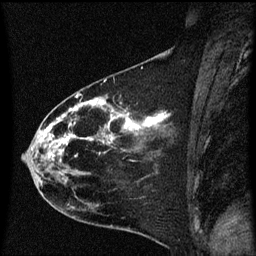
Breast MRI (dynamic contrast-enhanced), one sagittal slice. Slice 28 of 60 in the series (ordered by position). Dynamic contrast-enhanced series, image 2 of 3 at this slice position (ordered by acquisition). 1.5 T. TE 4.2 ms, TR 8.4 ms. 2 mm slice thickness. 256 × 256 image matrix. Patient: female, 35 years. Case-level facts recorded for this patient, not image findings: setting: breast cancer imaged before/during neoadjuvant chemotherapy; receptor status: HER2-positive.
Structures marked on this image (semi-automatically segmented with operator editing):
- analysis volume of interest (the breast-tissue region the enhancement analysis was run in; not a lesion): box from (x=22, y=68) to (x=174, y=173) px
- tumour enhancement mask (voxels above the 70 % enhancement threshold inside the analysis volume of interest): (x=36, y=94)–(x=166, y=173)